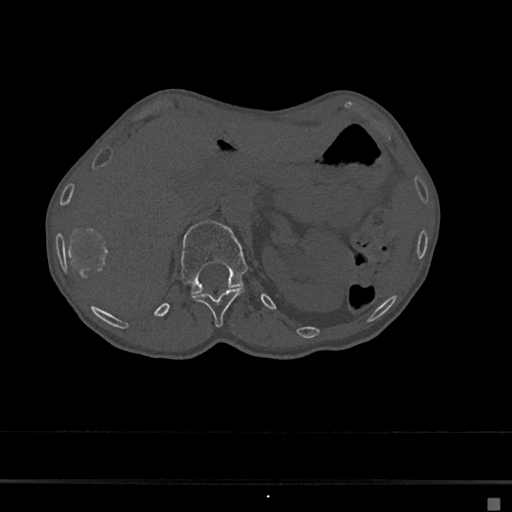
CT including the spine, one axial slice. Position 91 of 797 along the scan axis. Reconstruction kernel Br40s/3. Bone window (W 1800 / L 400 HU). 0.5 mm slice thickness. 512 × 512 image matrix, field of view 360 × 360 mm. Female patient, age 68 years. Case-level facts recorded for this patient, not image findings: primary cancer: renal.
Structures marked on this image (semi-automatically segmented with operator editing):
- L1 vertebra: bounding box <180,221,248,295> (left, top, right, bottom; pixels)
- T12 vertebra: <192,288,244,327>